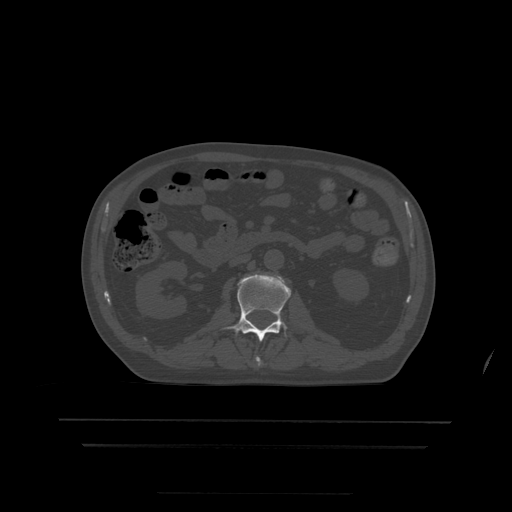
CT including the spine, one axial slice; position 144 of 522 along the scan axis; bone window (W 1800 / L 400 HU); 1.25 mm slice thickness; 512 × 512 image matrix. Patient age 68 years. From the clinical record (not read from this slice): primary cancer: urothelial.
Annotated regions visible in this slice (semi-automatically segmented with operator editing):
- L1 vertebra: bounding box <256,357,262,367> (left, top, right, bottom; pixels)
- L2 vertebra: <223,274,292,342>